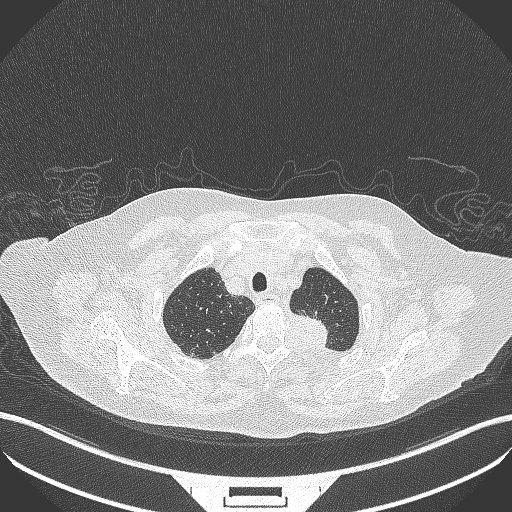
Chest CT, one axial slice; slice 302 of 353 in the series (ordered by position); reconstruction kernel B70f; 100 kVp; lung window (W 1500 / L -600 HU); 512 × 512 image matrix. Female patient, age 81 years. Case-level facts recorded for this patient, not image findings: clinical TNM (as recorded): T2a N0 M0.
Outlined on this slice (bounding box drawn by a radiologist):
- lung tumour (recorded histology: adenocarcinoma): bounding box <272,301,338,349> (left, top, right, bottom; pixels)